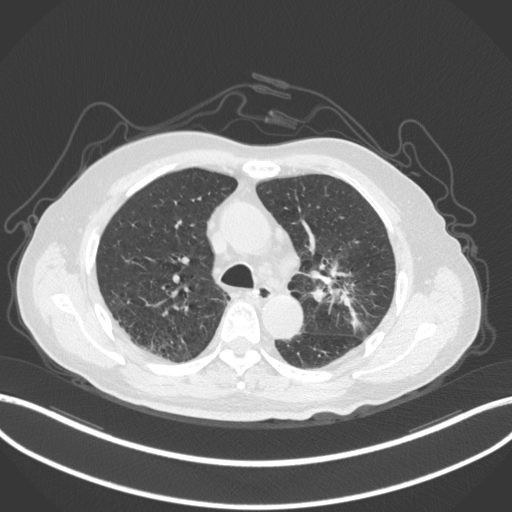
Chest CT, one axial slice. Reconstruction kernel B31f. Lung window (W 1500 / L -600 HU). 512 × 512 image matrix, field of view 400 × 400 mm. Male patient, age 79 years. From the clinical record (not read from this slice): clinical TNM (as recorded): T2a N1 M1.
Annotated regions visible in this slice (rectangle marked by the reading radiologist):
- lung tumour (recorded histology: adenocarcinoma): bounding box [x1, y1, x2, y2] px = [316, 267, 369, 336]